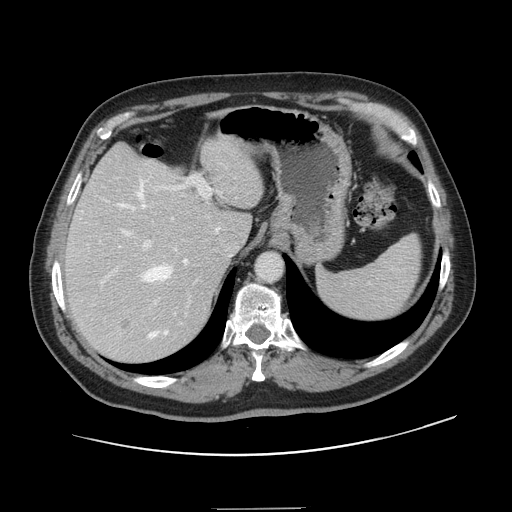
Contrast-enhanced abdominal CT, one axial slice; position 104 of 143 along the scan axis; 120 kVp; intravenous contrast given; soft-tissue window (W 400 / L 40 HU); 512 × 512 image matrix, field of view 402 × 402 mm. Male patient, age 62 years. Case-level facts recorded for this patient, not image findings: diagnosis: colorectal cancer liver metastases, imaged before liver resection; multiple liver metastases: yes; largest metastasis: 2.7 cm; disease in both lobes: no.
Outlined on this slice (manually delineated by an expert):
- hepatic veins: bounding box [x1, y1, x2, y2] px = [100, 180, 188, 338]
- liver: [67, 139, 263, 361]
- planned liver remnant (the part of the liver to remain after resection): [67, 138, 263, 268]
- portal vein (with intrahepatic branches): [102, 175, 212, 285]
- liver metastasis: [123, 322, 130, 329]